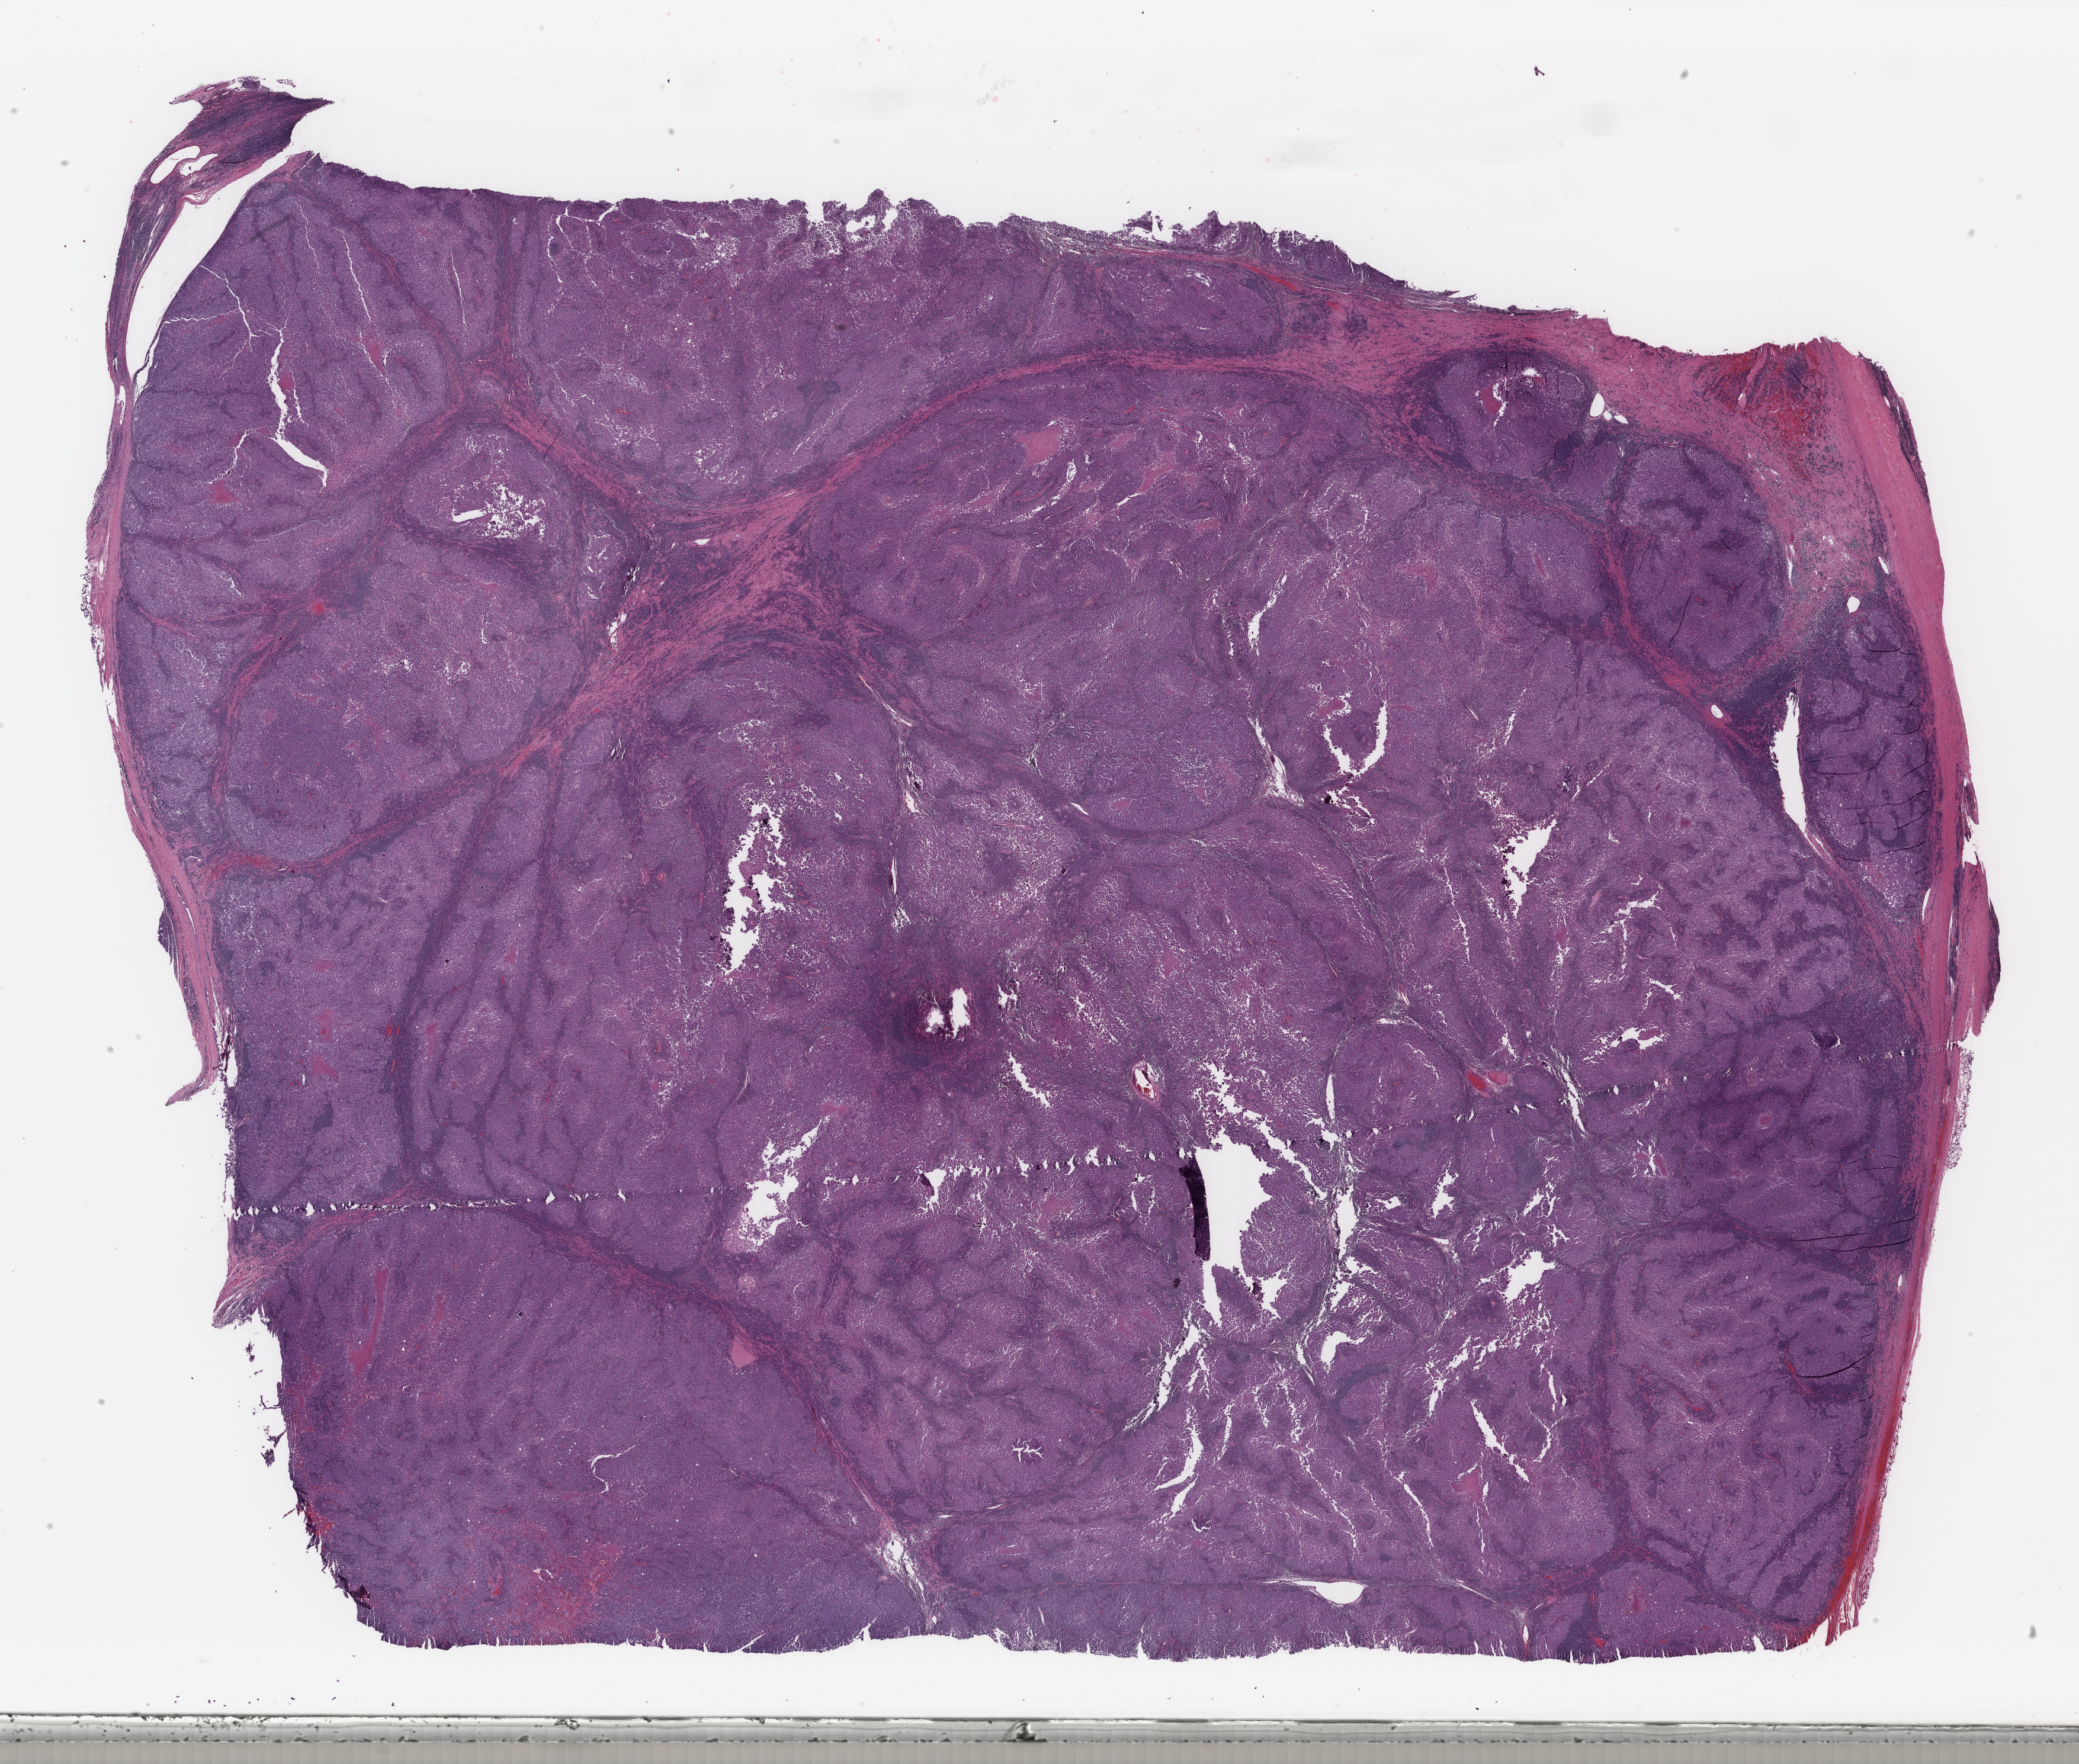
H&E whole-slide image, shown as a low-resolution overview of the whole scanned area (about 27.9 x 23.6 mm), formalin-fixed paraffin-embedded (FFPE) diagnostic section, skin, primary tumour sample. Female patient; age at initial diagnosis 81 years.
Diagnosis: Malignant melanoma, NOS.